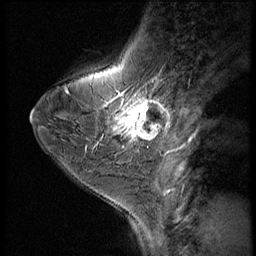
Breast MRI (dynamic contrast-enhanced), one sagittal slice. Dynamic contrast-enhanced series, image 2 of 3 at this slice position (ordered by acquisition). 1.5 T. TE 4.2 ms, TR 9 ms. 2.5 mm slice thickness. 256 × 256 image matrix, field of view 180 × 180 mm. Patient: female, 38 years. From the clinical record (not read from this slice): setting: breast cancer imaged before/during neoadjuvant chemotherapy; receptor status: triple-negative.
Outlined on this slice (semi-automatically segmented with operator editing):
- analysis volume of interest (the breast-tissue region the enhancement analysis was run in; not a lesion): bounding box <107,95,173,149> (left, top, right, bottom; pixels)
- tumour enhancement mask (voxels above the 140 % enhancement threshold inside the analysis volume of interest): <114,95,169,141>